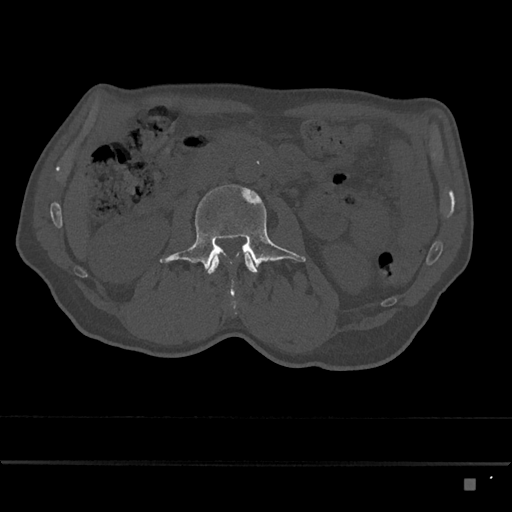
CT including the spine, one axial slice. Position 424 of 797 along the scan axis. Reconstruction kernel Br40s/3. 120 kVp. Bone window (W 1800 / L 400 HU). 0.5 mm slice thickness. 512 × 512 image matrix, field of view 390 × 390 mm. Male patient, age 72 years. Case-level facts recorded for this patient, not image findings: primary cancer: prostate.
Structures marked on this image (semi-automatically segmented with operator editing):
- L2 vertebra: bounding box (x1, y1, x2, y2) in pixels: (207, 253, 257, 274)
- L3 vertebra: (160, 184, 306, 297)